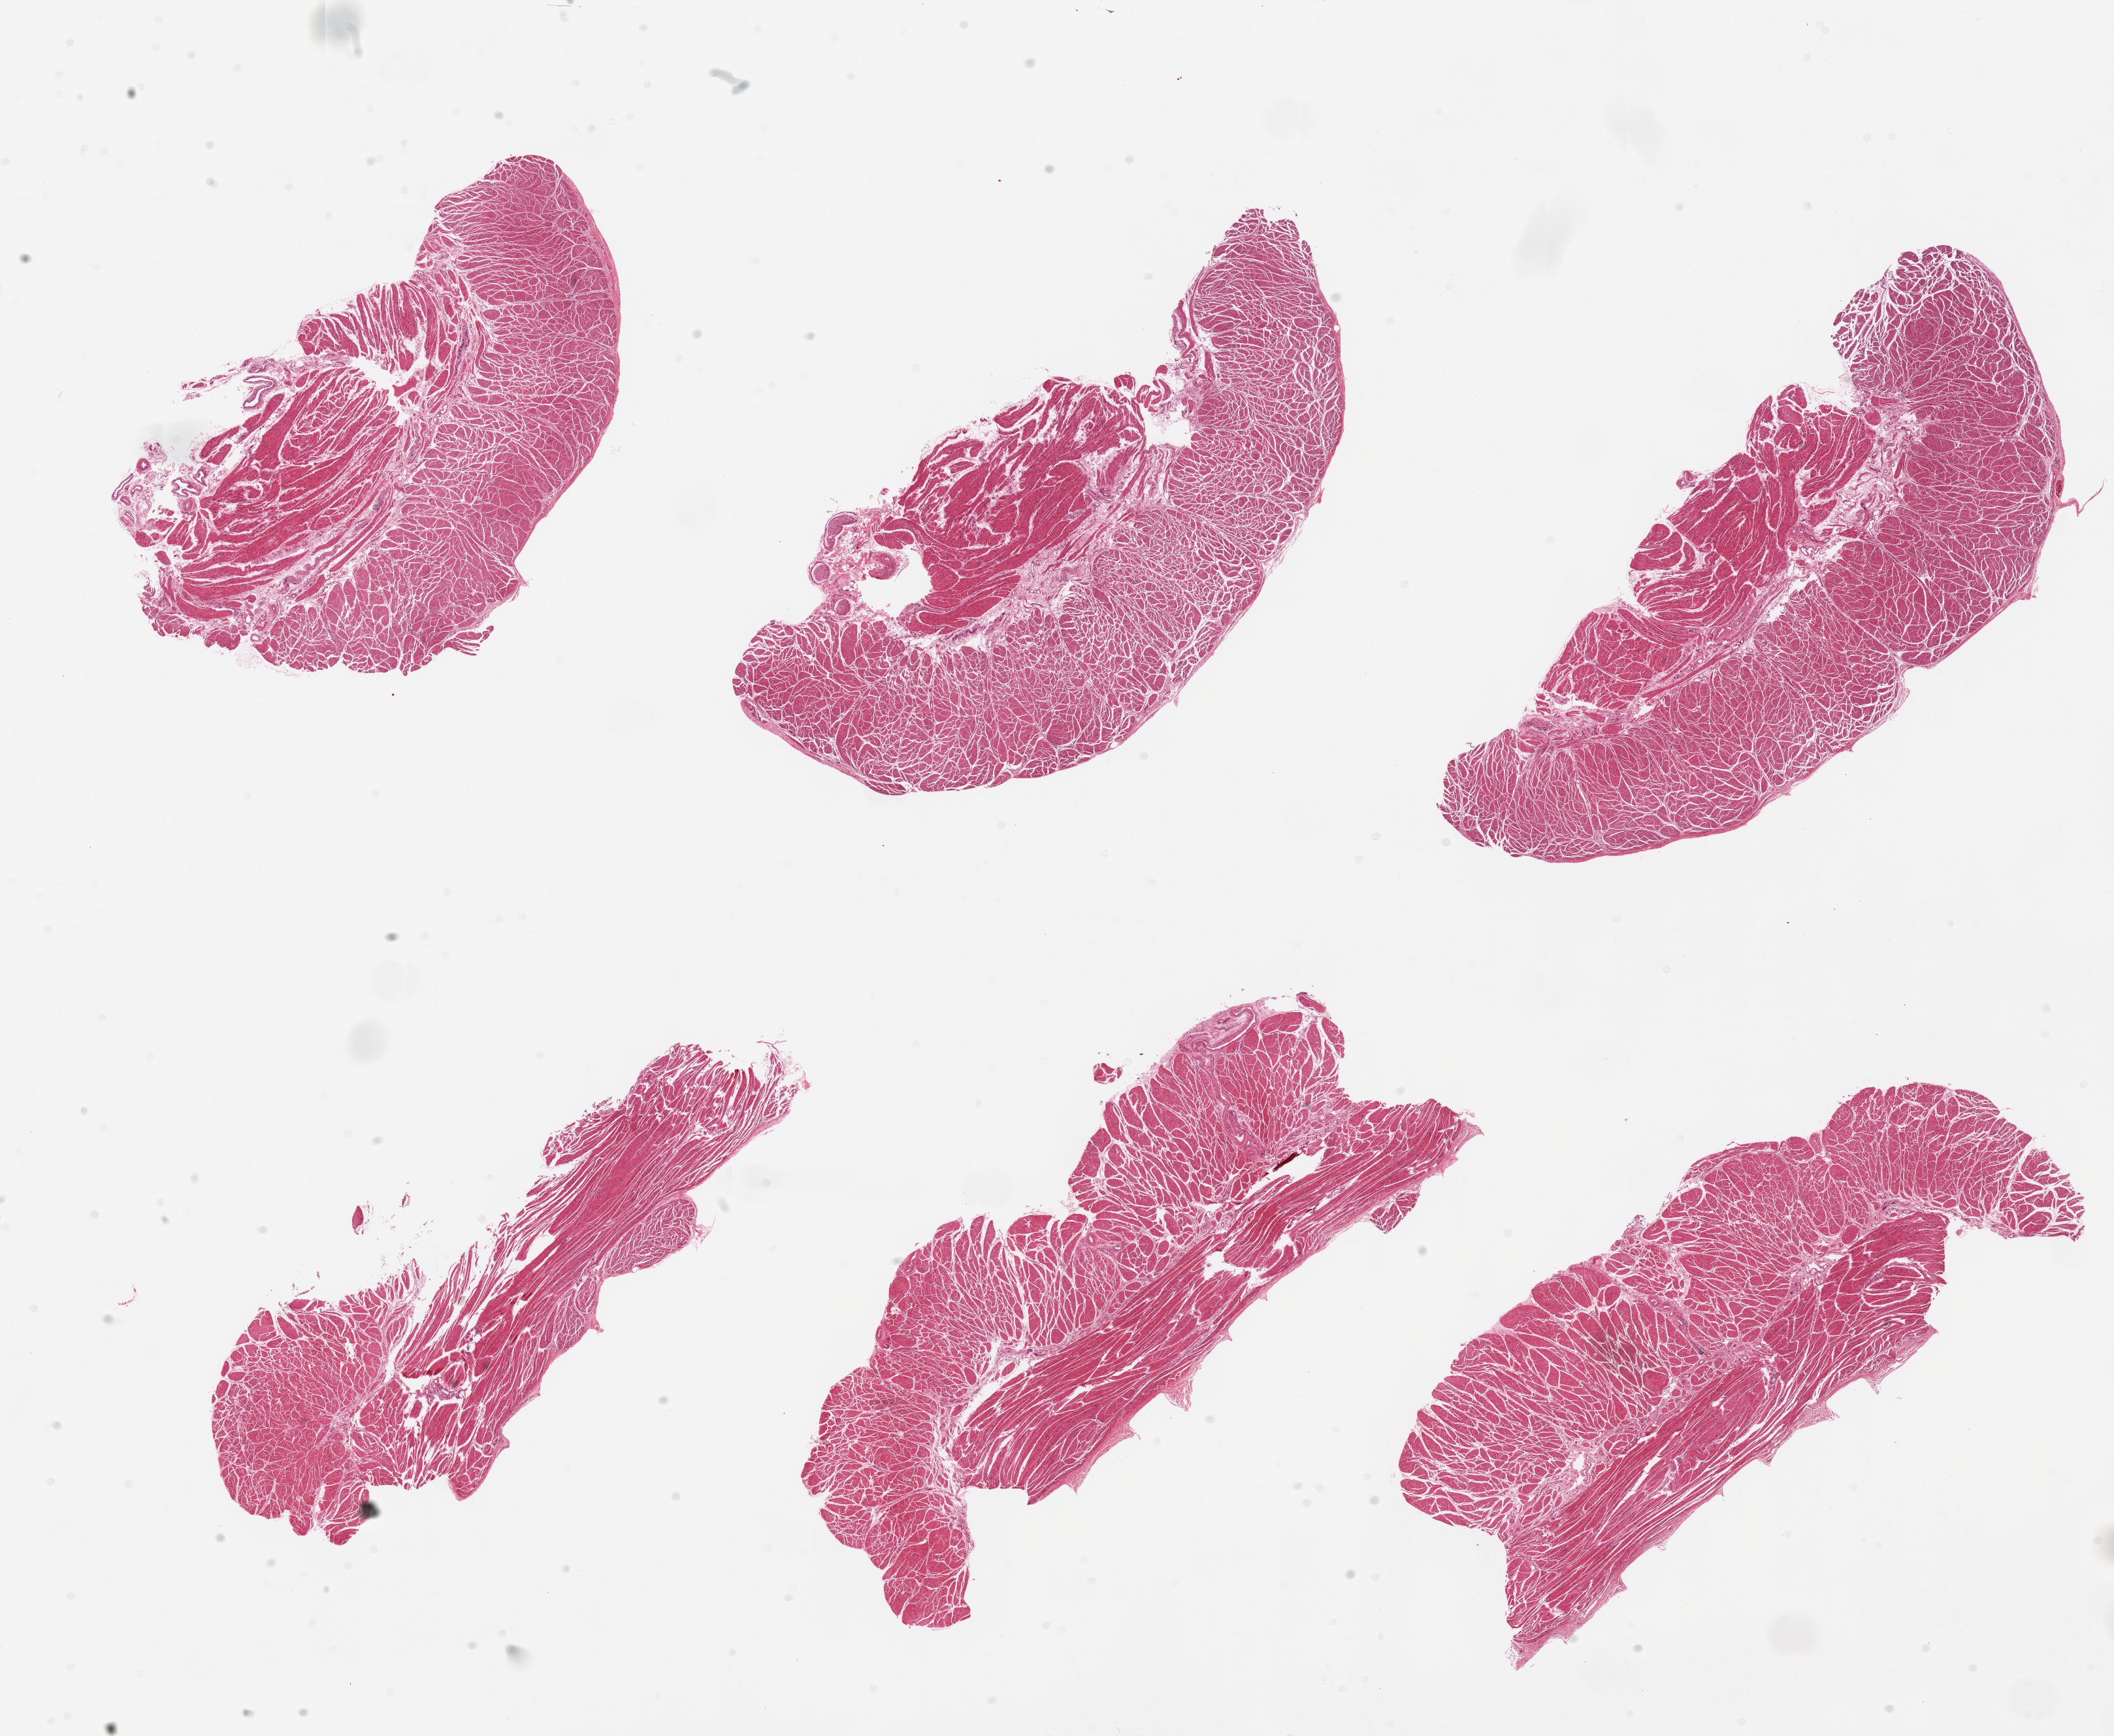
Haematoxylin and eosin whole-slide image, shown as a low-resolution overview of the whole scanned area (about 25.6 x 21.0 mm, acquisition: 20x scan), PAXgene-fixed, paraffin-embedded tissue, target tissue: esophageal muscle, donor tissue sample. Donor: female.
• pathologist's review note for this sample: 6 pieces